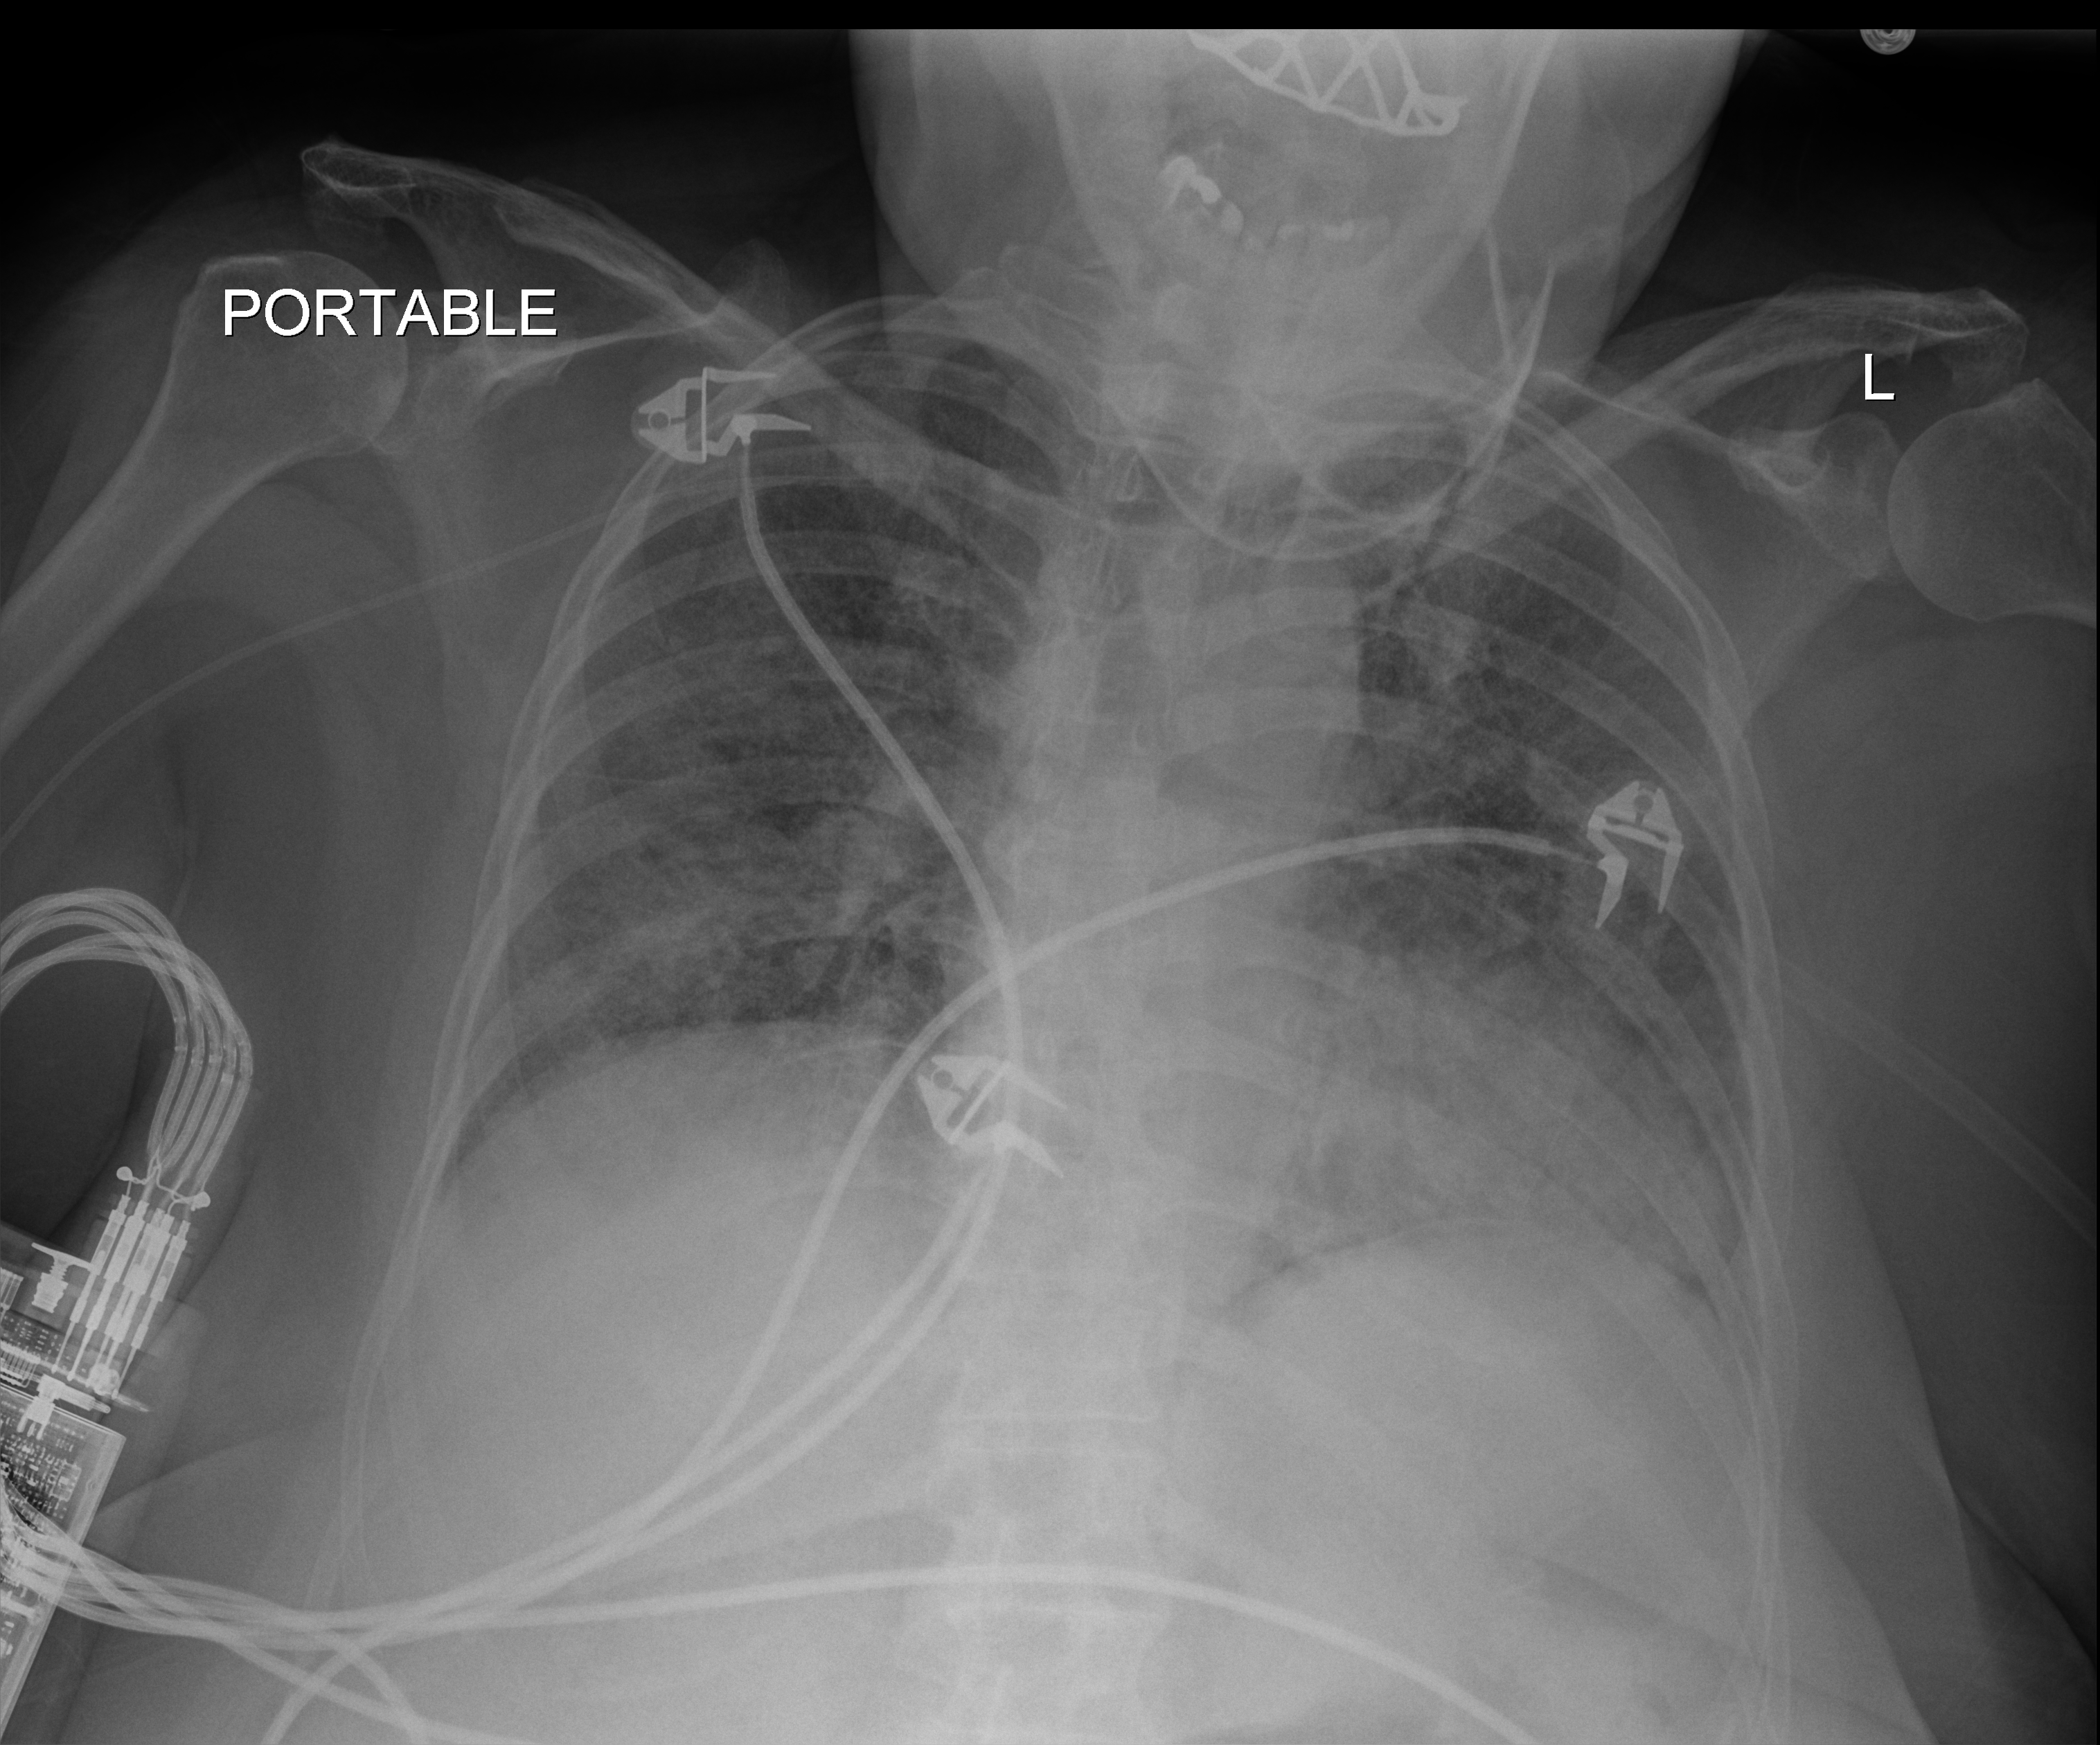
Bedside chest radiograph (digital radiography), anteroposterior (AP) projection. Female patient hospitalised with COVID-19, age 60–74 years.
Hospital-stay facts (about this admission, not read from this image; timing relative to this image not recorded):
- diabetes (admission record): no
- admitted to intensive care during this hospital stay: yes
- COPD (admission record): no